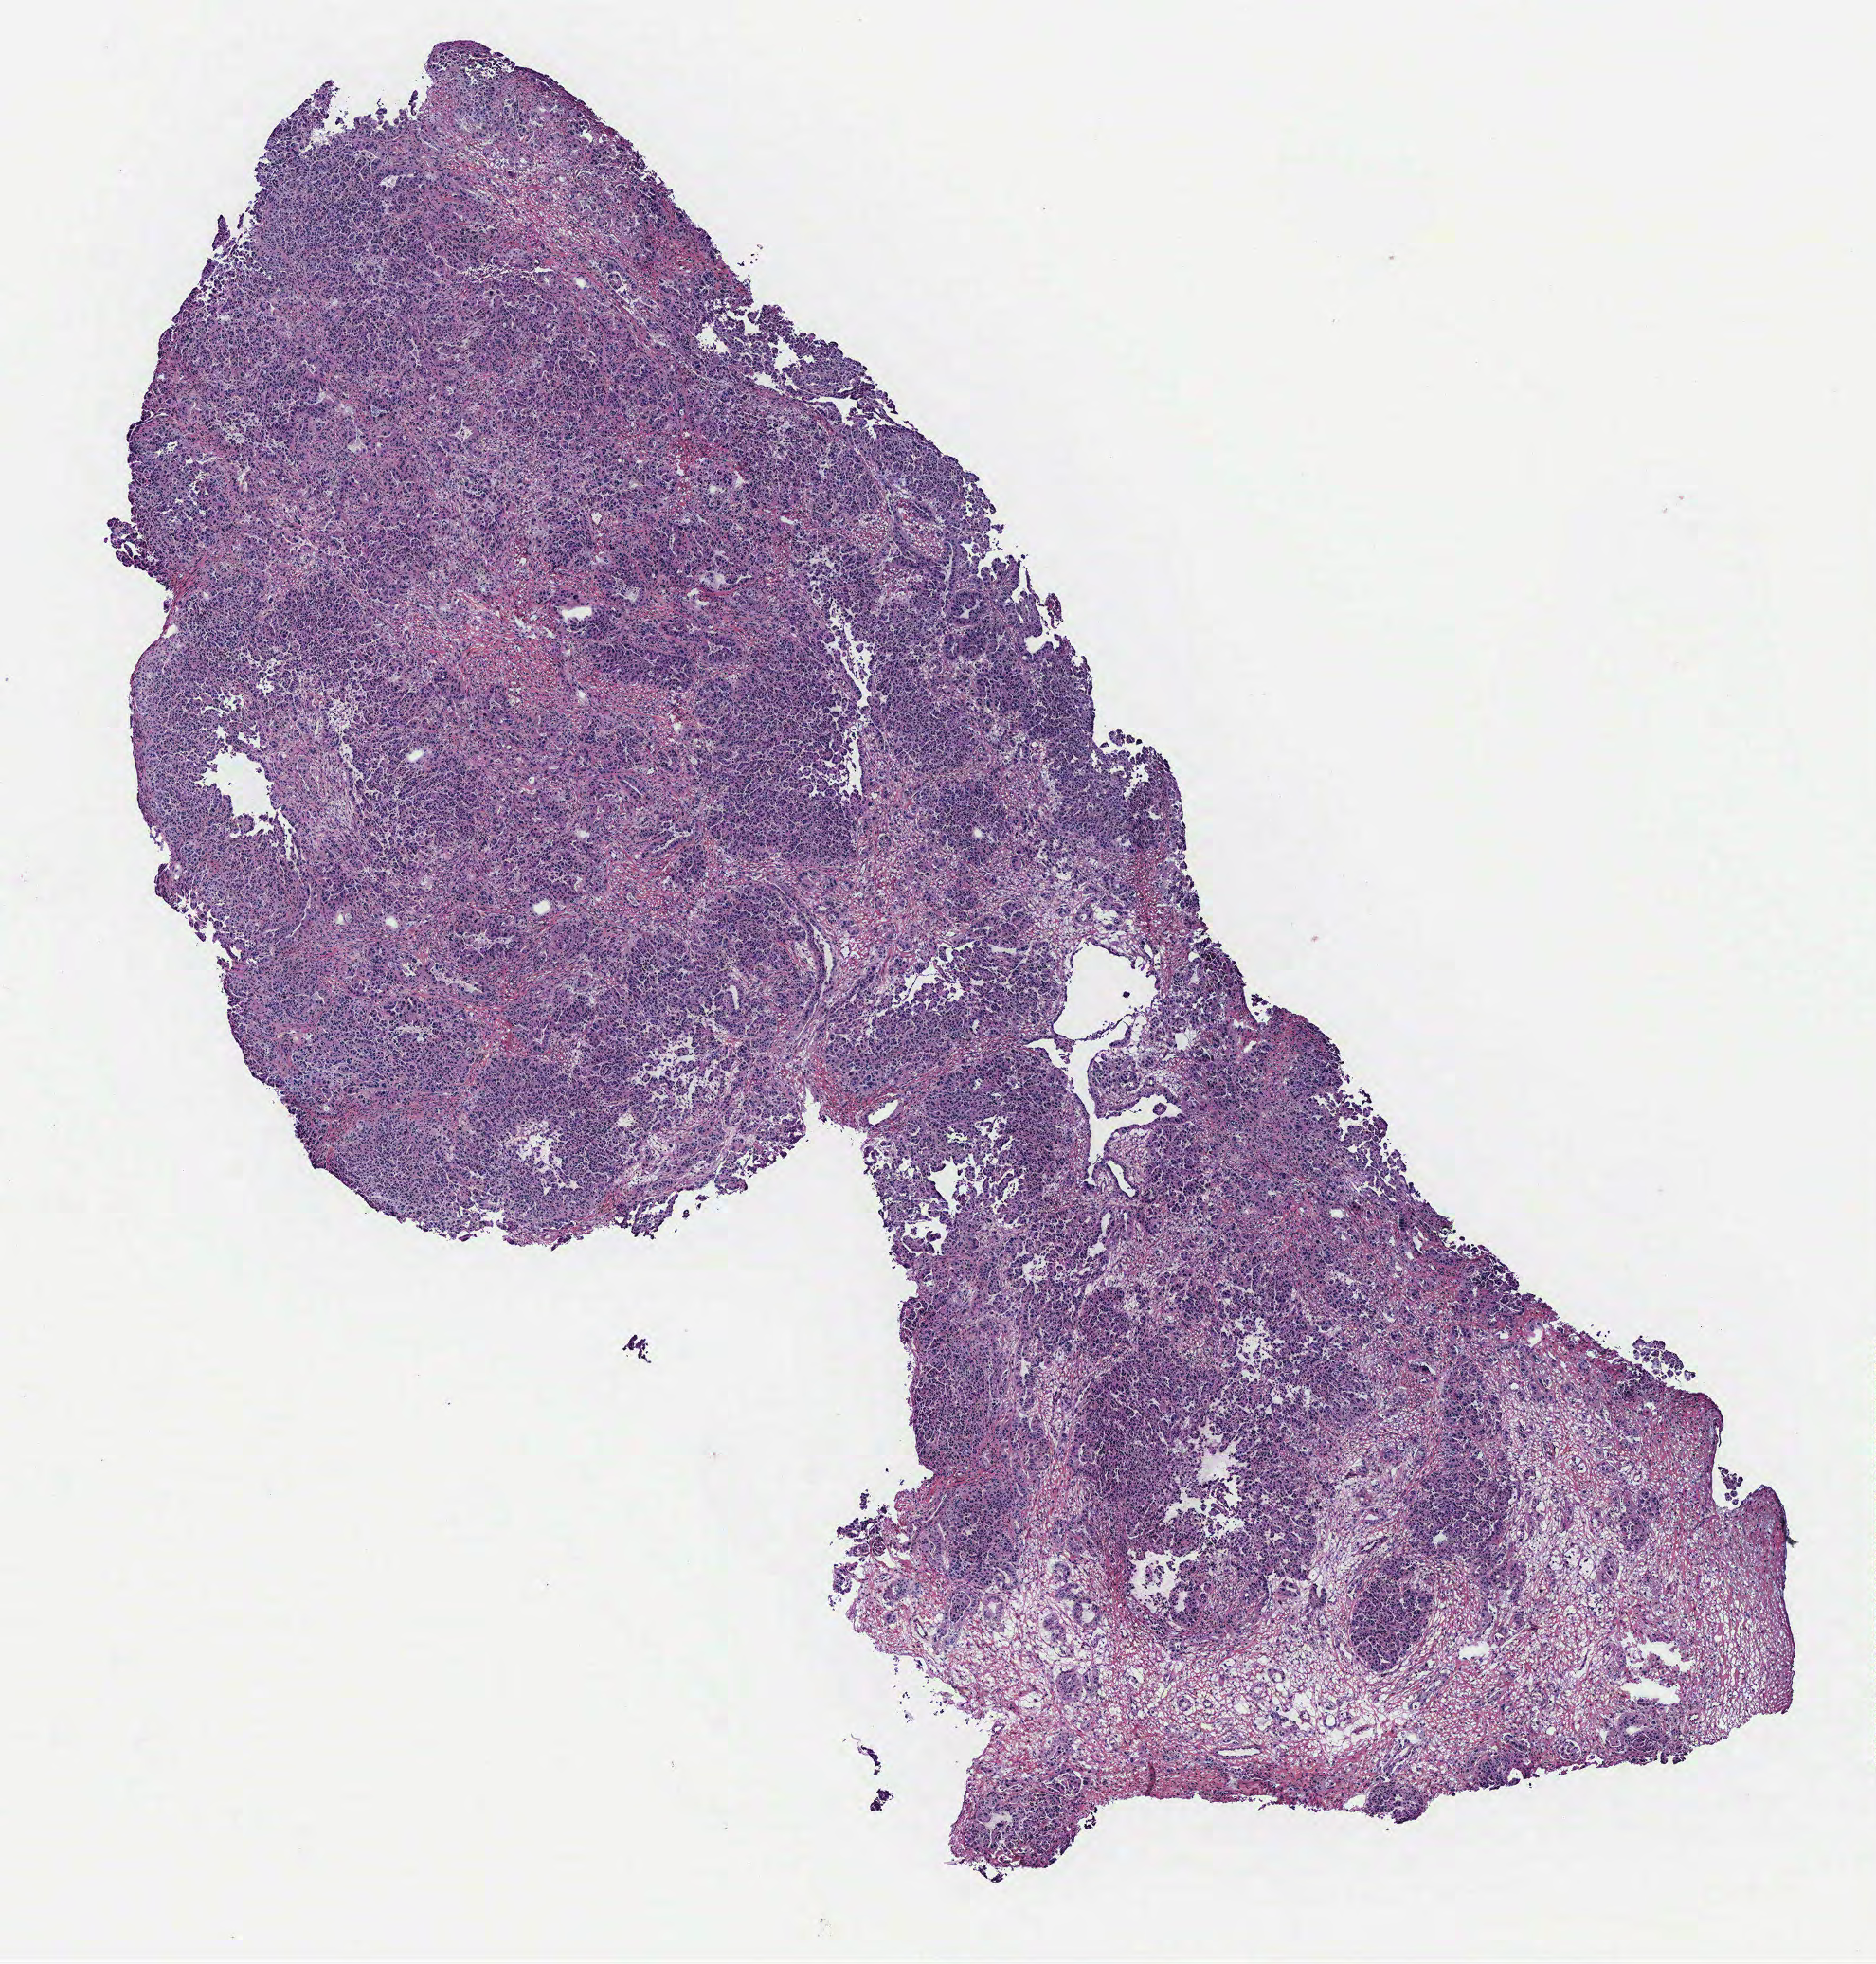
Whole-slide histology image, Hematoxylin and eosin (H&E) stained, a low-resolution overview of the entire scanned area, about 7.9 x 8.3 mm (from a 40x scan). Ovary, tumour tissue. 58-year-old female patient.
Primary tumour site (as recorded): ovary. Diagnosis: Serous adenocarcinoma, NOS.